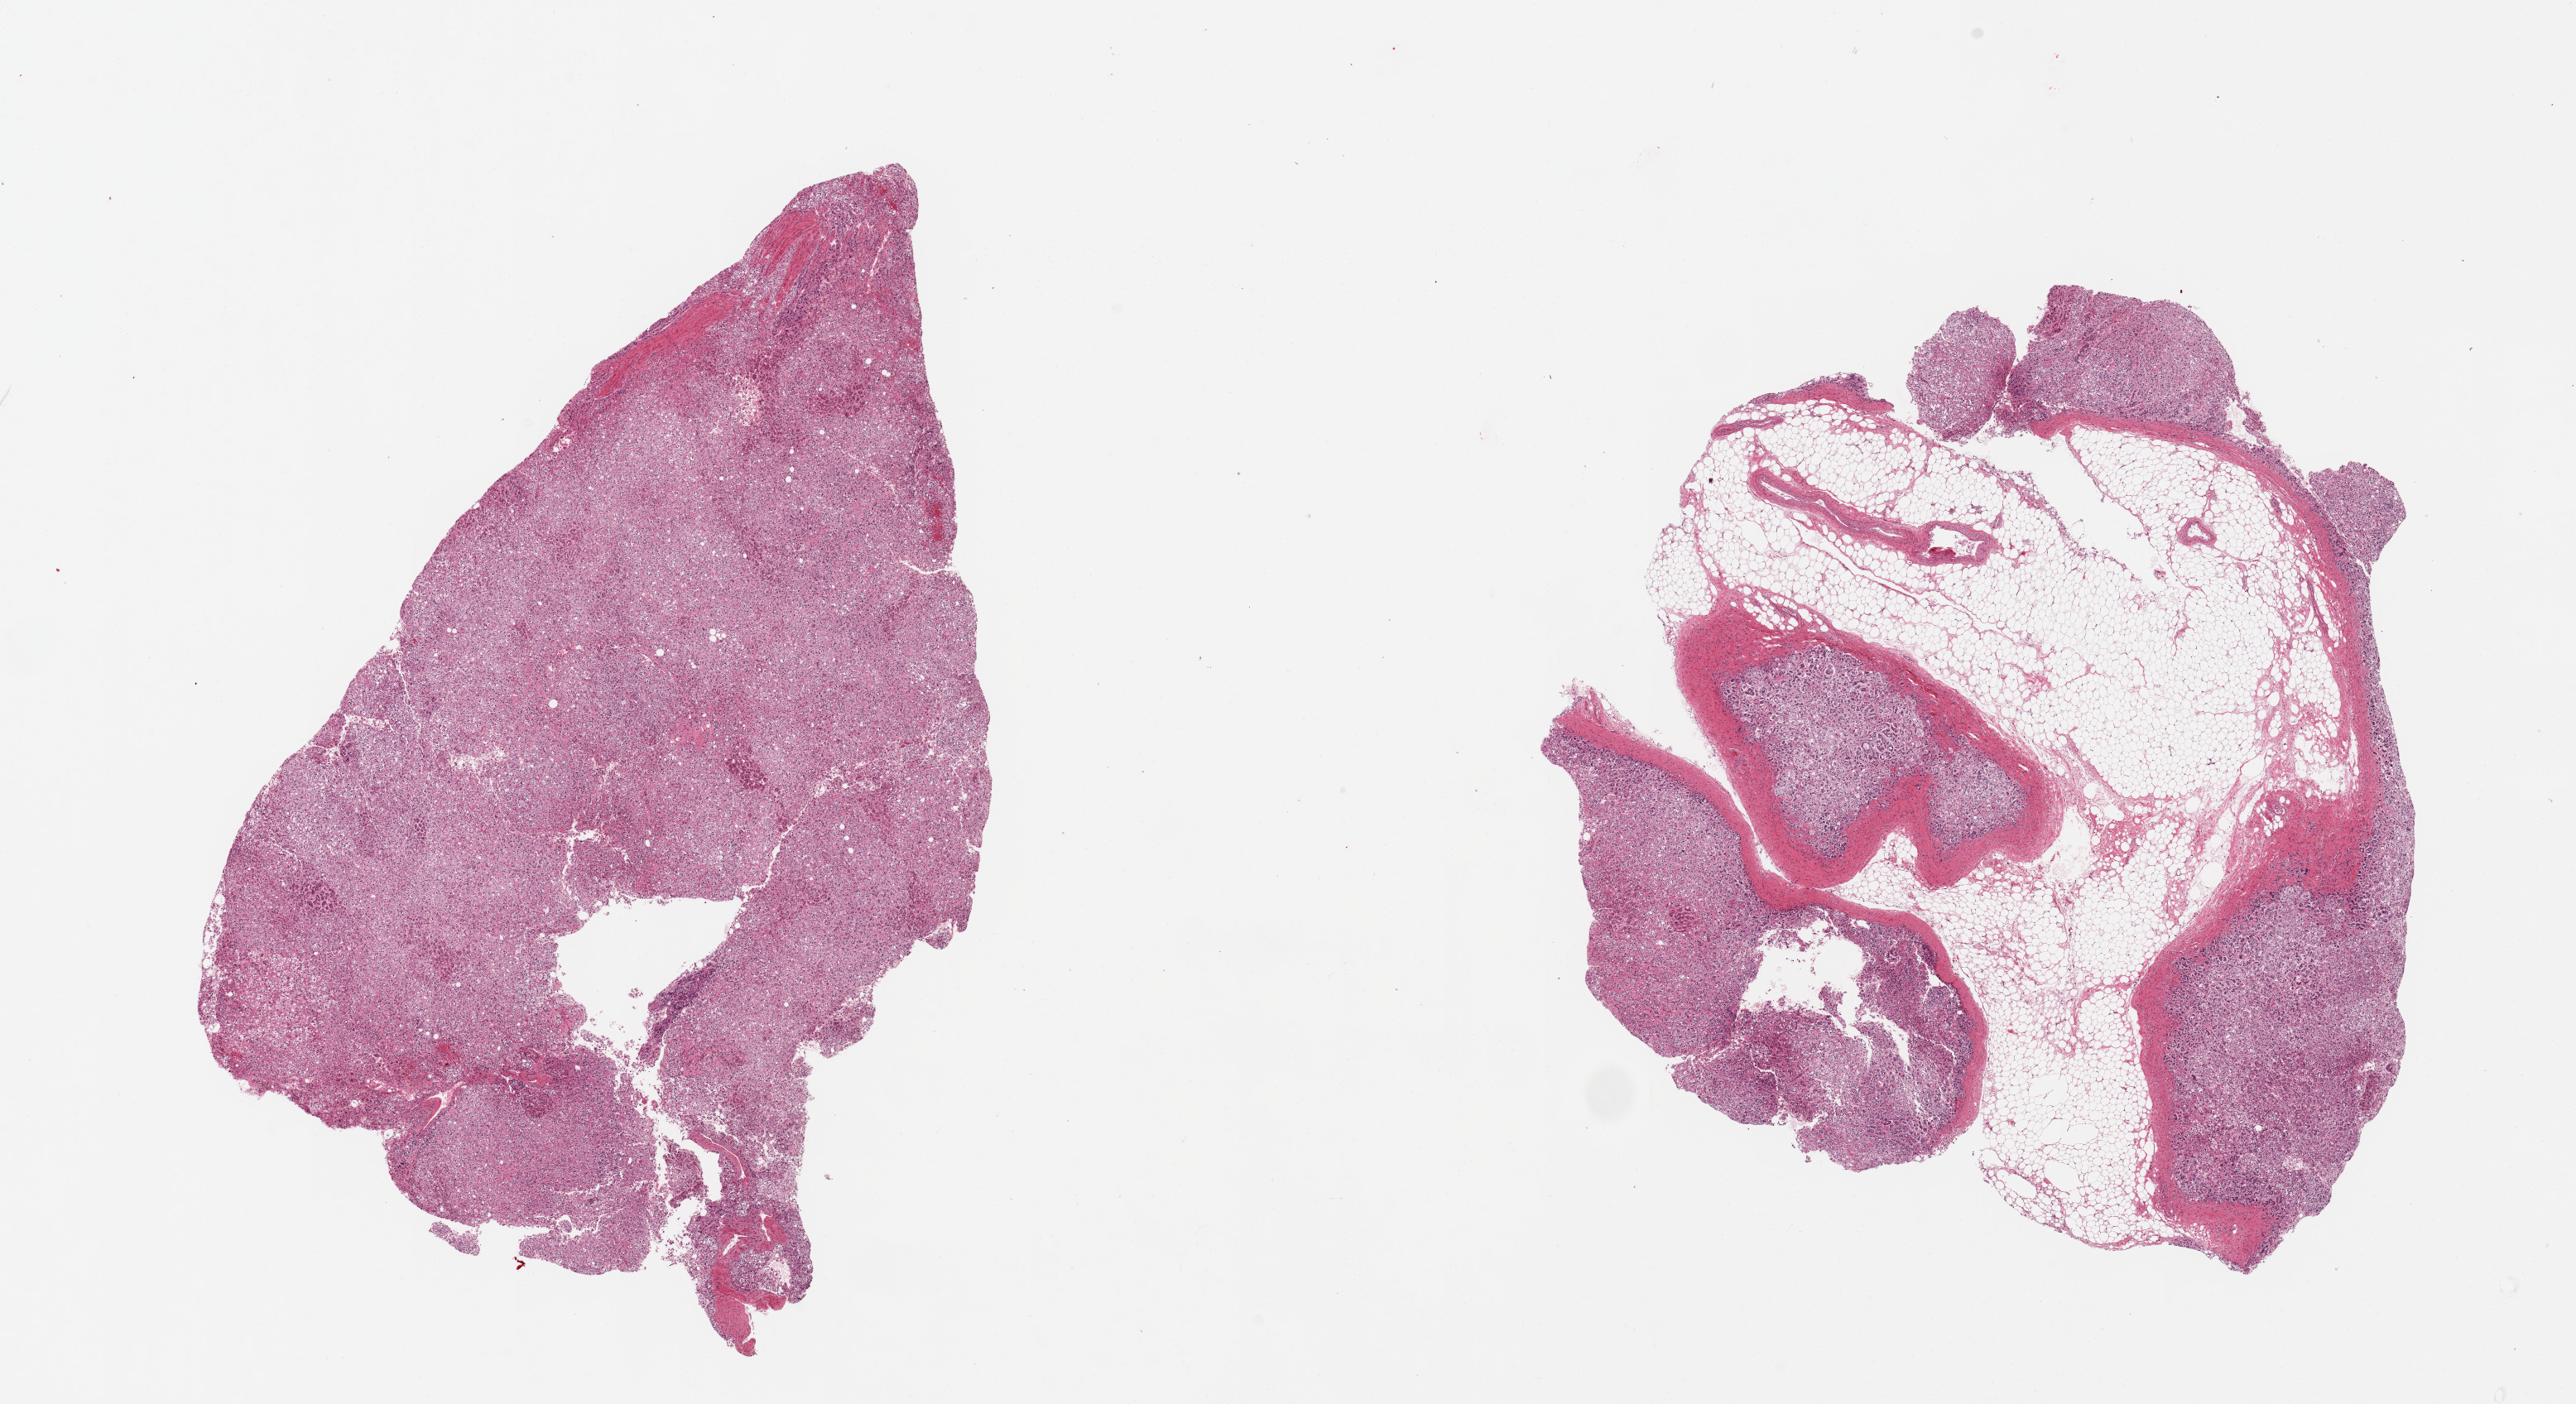
Digitized hematoxylin and eosin (H&E)-stained section, brightfield, whole scanned area (about 24.6 x 13.4 mm) shown as a low-resolution overview. PAXgene-fixed paraffin-embedded (PFPE) section. Section of adrenal gland (target tissue). Tissue donor sample. Donor sex: male.
Reviewer comment on this tissue sample: 2 pieces; 1 has 50% internal fat; other is fat-free.